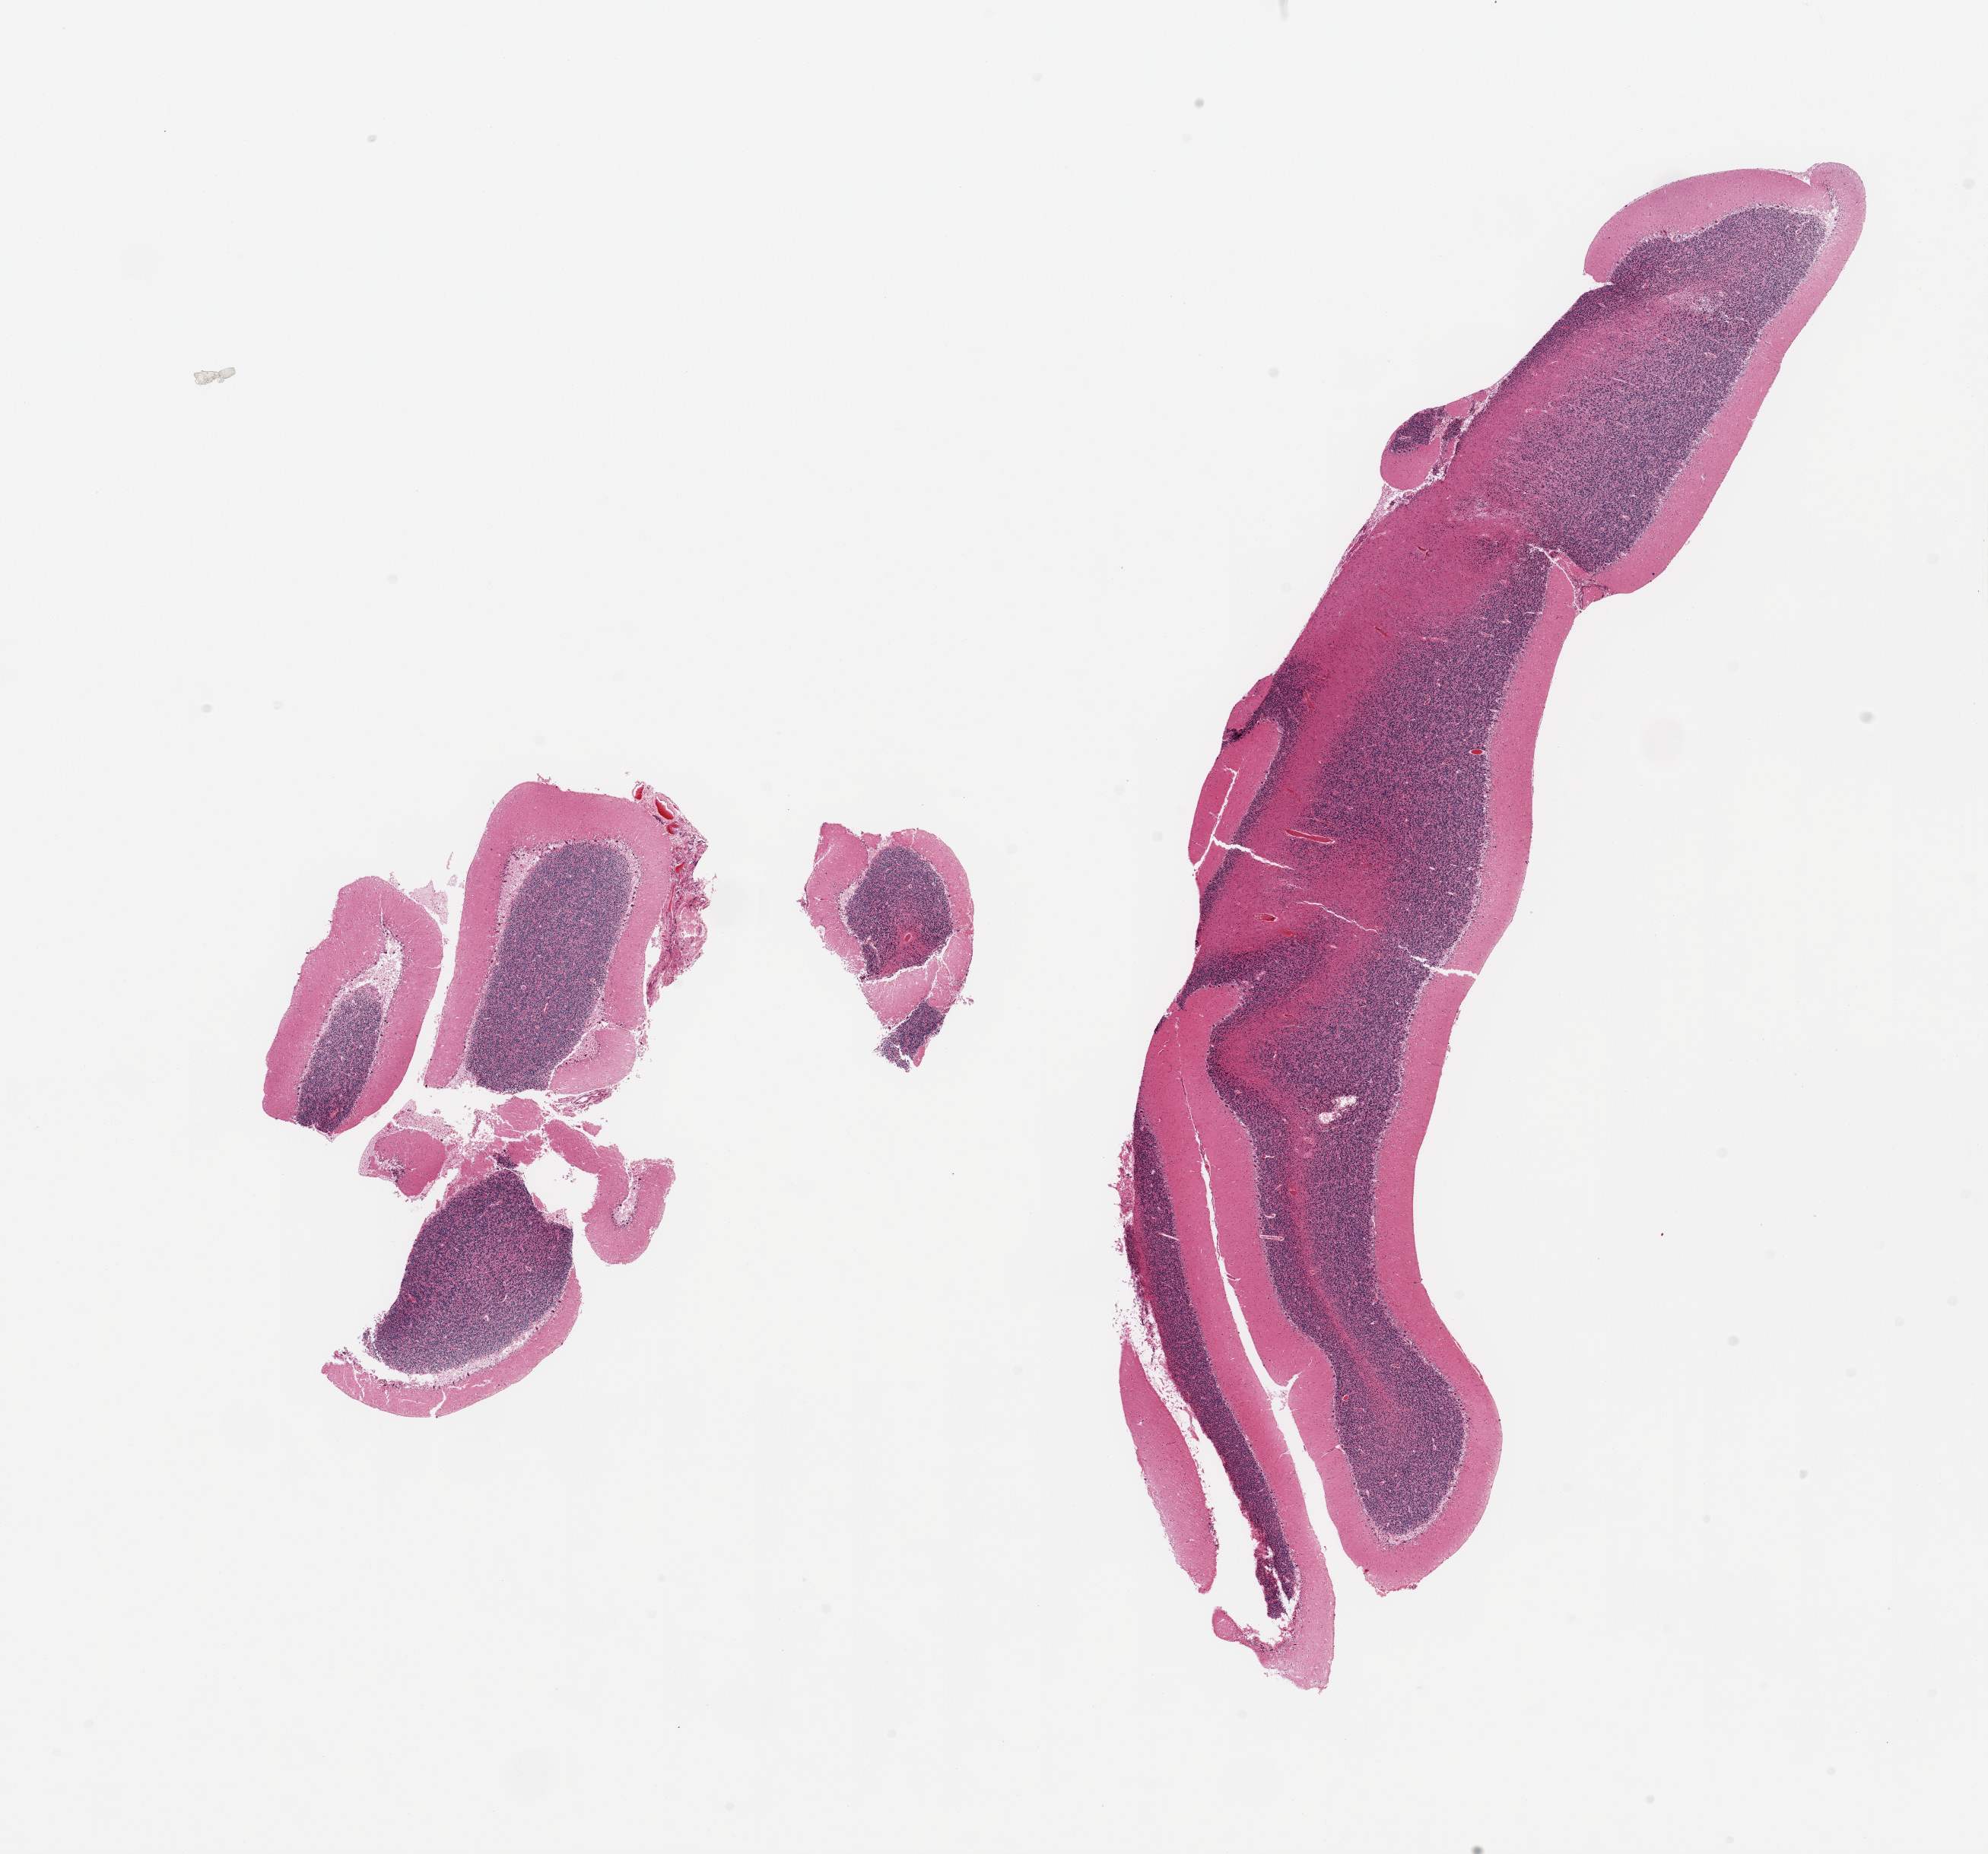
Haematoxylin and eosin whole-slide image, low-resolution overview of the scanned area, about 20.7 x 19.3 mm; PAXgene-fixed, paraffin-embedded tissue; section of cerebellum (target tissue); tissue donor sample.
- pathologist's review note for this sample: 1 large & 1 small fragmented piece